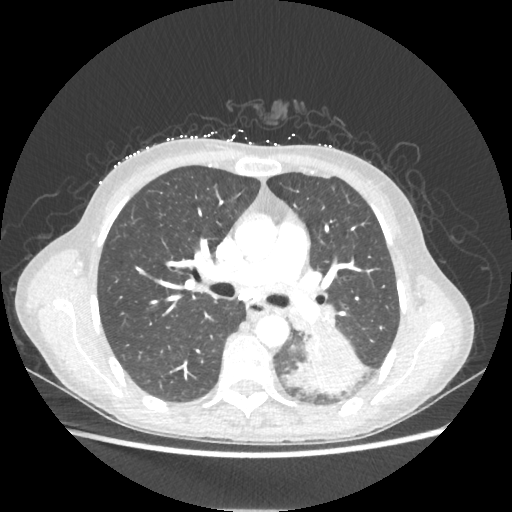
Chest CT, one axial slice; position 132 of 221 along the scan axis; reconstruction kernel STANDARD; lung window (W 1500 / L -600 HU); 1.25 mm slice thickness; 512 × 512 image matrix, field of view 360 × 360 mm. Patient: female, 53 years. Case-level facts recorded for this patient, not image findings: clinical TNM (as recorded): T3 N0 M0.
Structures marked on this image (bounding box drawn by a radiologist):
- lung tumour (recorded histology: adenocarcinoma): bounding box (x1, y1, x2, y2) in pixels: (290, 329, 365, 395)